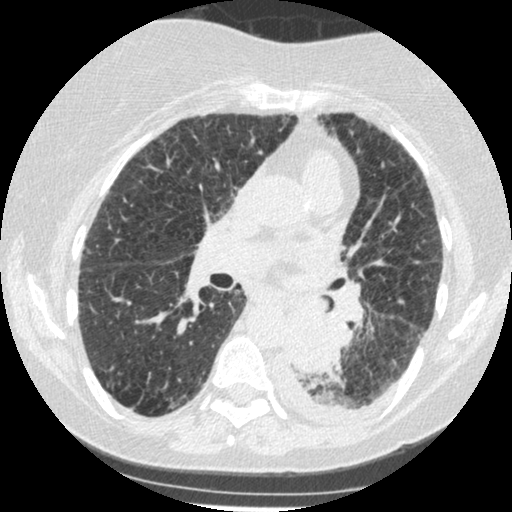
Low-dose screening chest CT, one axial slice; position 136 of 341 along the scan axis; reconstruction kernel STANDARD; lung window (W 1500 / L -600 HU); 512 × 512 image matrix.
Outlined on this slice (outlined manually by an expert reader):
- lesion 1 (tumor, lower lobe of left lung): box from (x=285, y=309) to (x=340, y=374) px